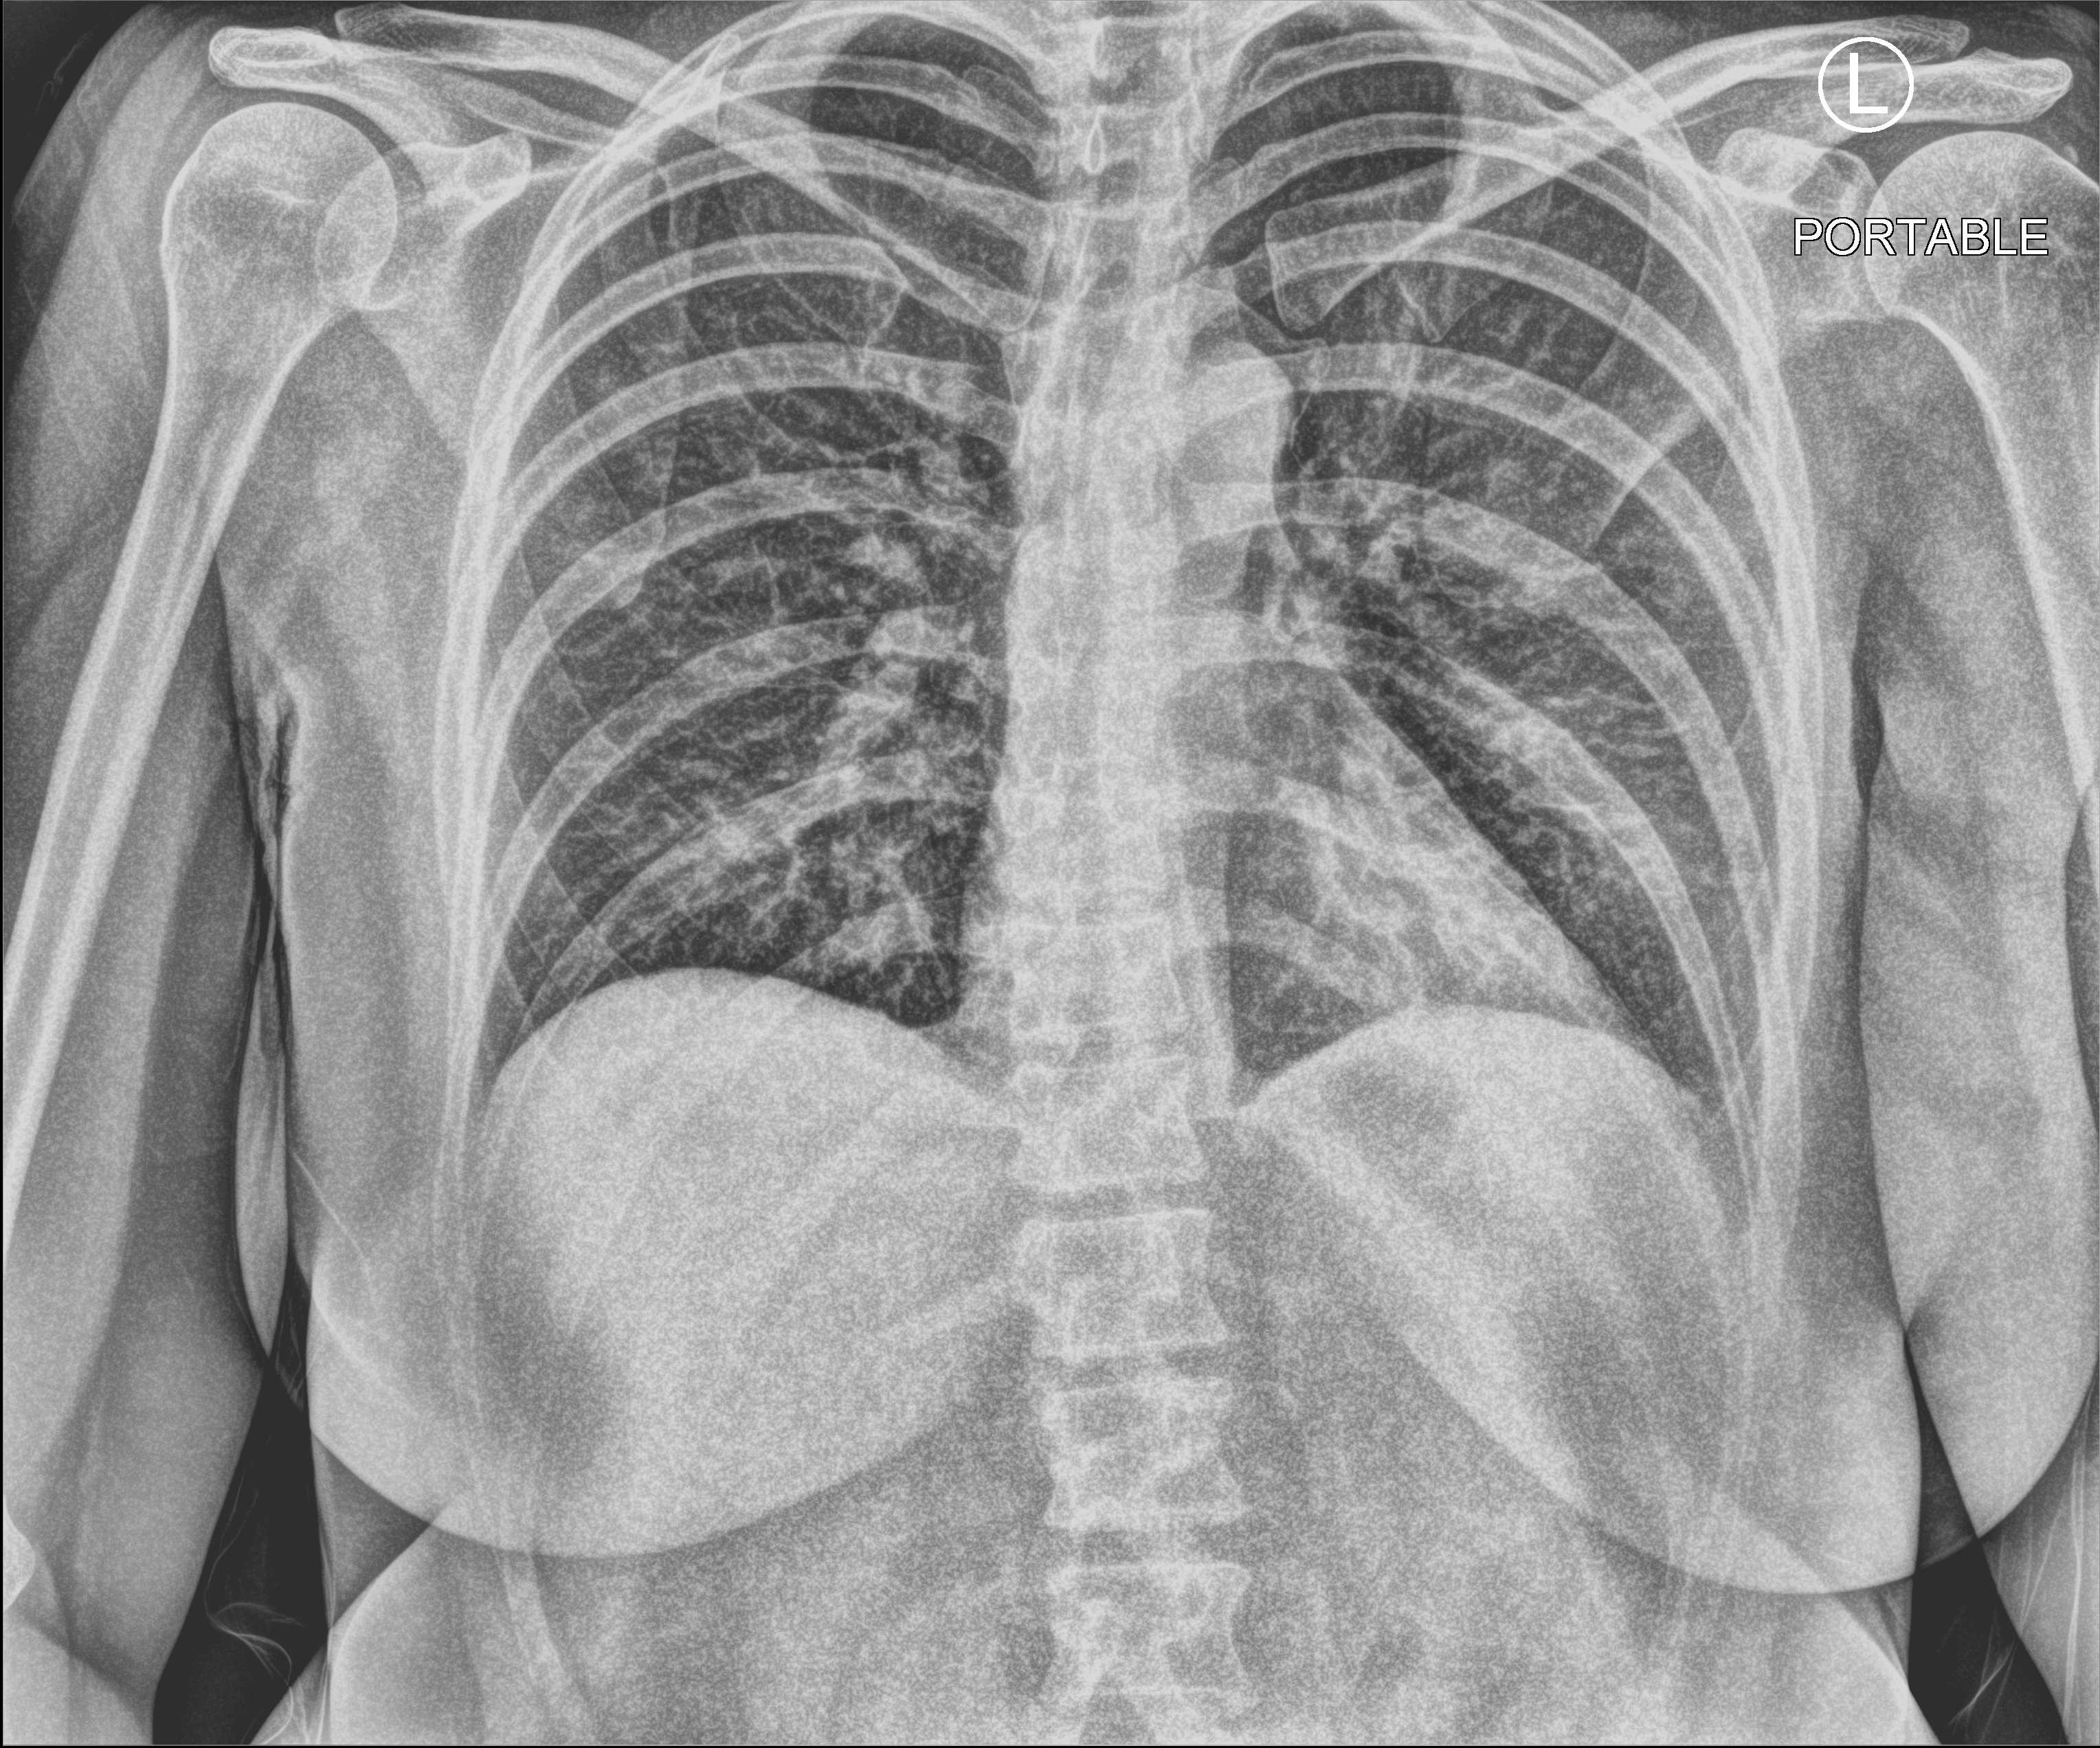
Bedside chest radiograph (computed radiography), anteroposterior (AP) projection. Female patient hospitalised with COVID-19, age 18–59 years.
Admission-level facts for this patient (not findings on this image; timing relative to this image not recorded): mechanically ventilated during this hospital stay: no; admitted to intensive care during this hospital stay: no; chronic kidney disease (admission record): no.